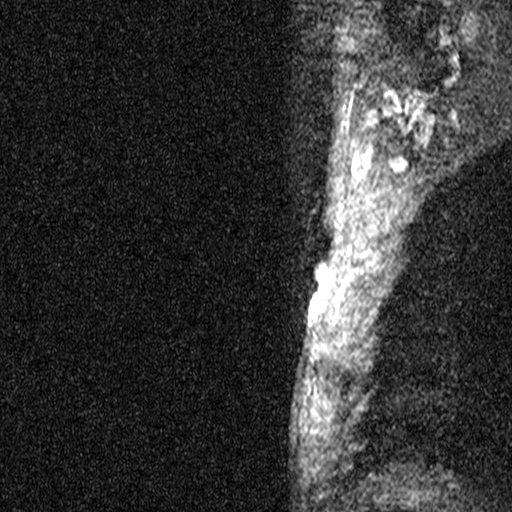
Breast MRI (dynamic contrast-enhanced), one sagittal slice; position 38 of 44 along the scan axis; dynamic contrast-enhanced study with each time point stored as its own series, time point 2 of 3 at this slice position (early post-contrast, ordered by acquisition time); 1.5 T; TE 4.5 ms, TR 11 ms; 3 mm slice thickness; 512 × 512 image matrix, field of view 200 × 200 mm. Patient: female, 45 years. From the clinical record (not read from this slice): setting: breast cancer imaged before/during neoadjuvant chemotherapy; receptor status: HR-positive, HER2-negative.
Outlined on this slice (semi-automatic segmentation, software-assisted and operator-edited):
- analysis volume of interest (the breast-tissue region the enhancement analysis was run in; not a lesion): bounding box <256,218,351,359> (left, top, right, bottom; pixels)
- tumour enhancement mask (voxels above the 90 % enhancement threshold inside the analysis volume of interest): <310,303,313,307>